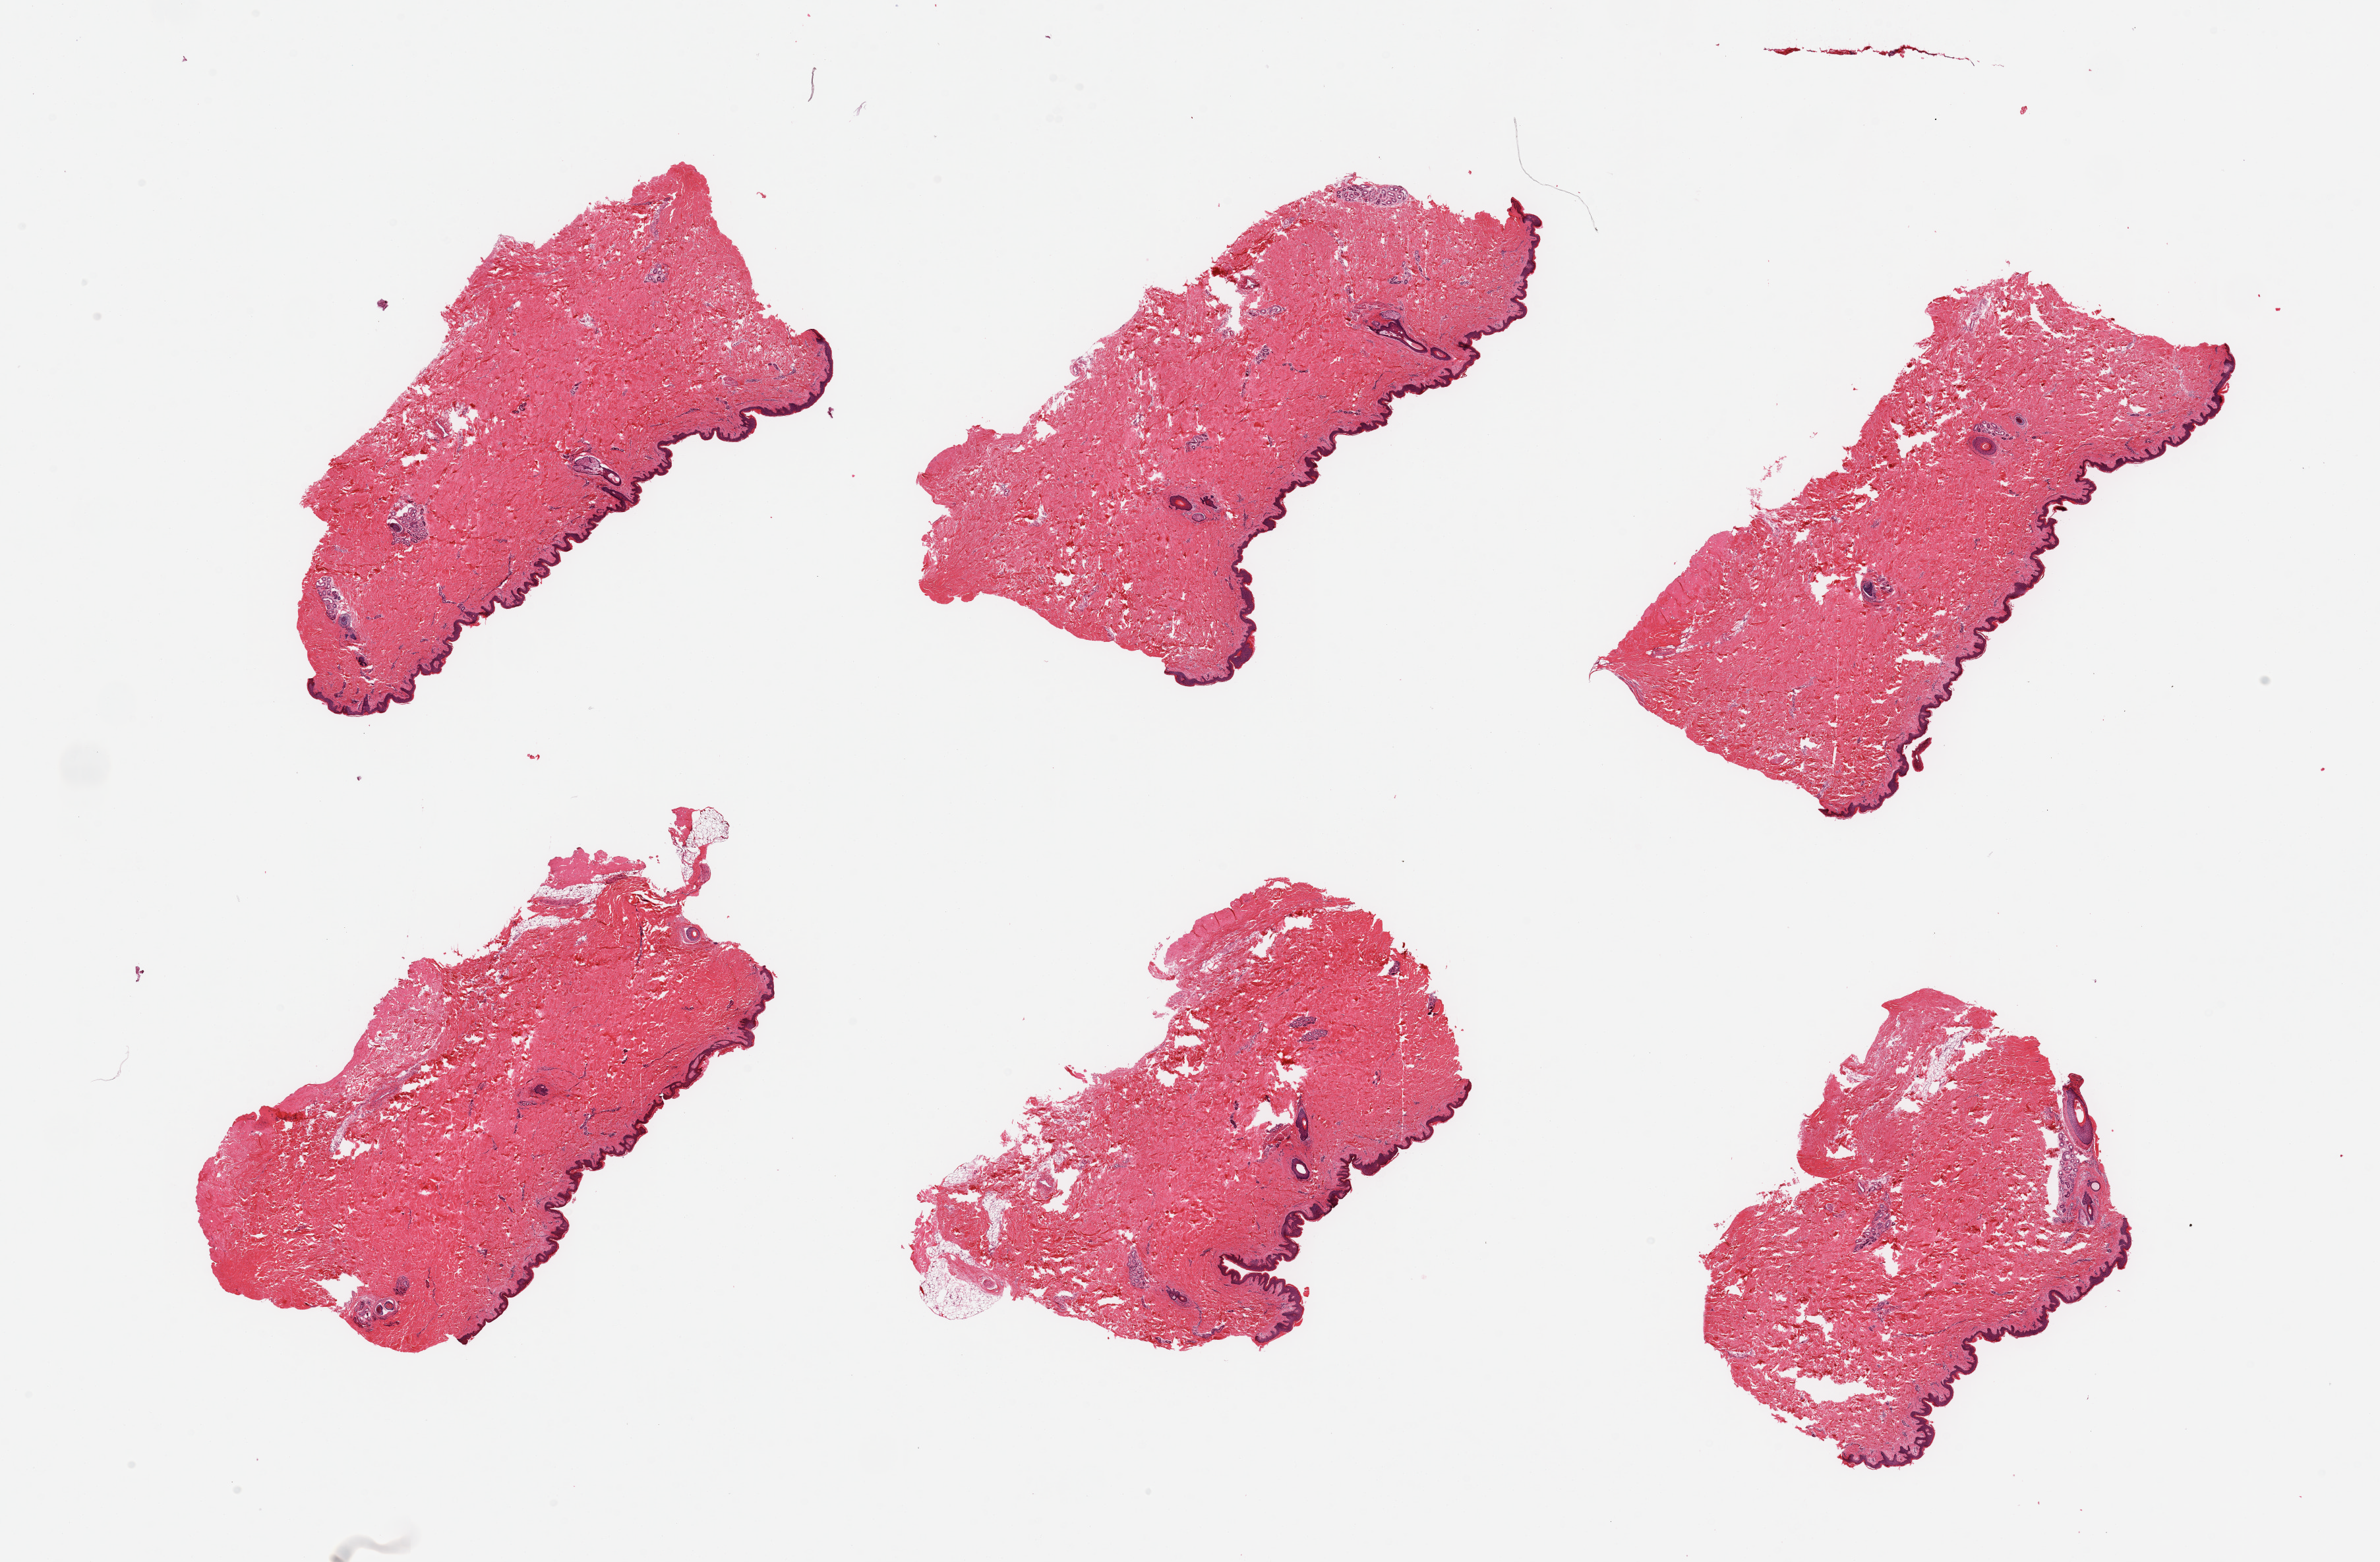
H&E whole-slide image — a low-resolution overview of the entire scanned area, about 28.5 x 18.7 mm; PAXgene-fixed paraffin-embedded (PFPE) section; target tissue: skin of suprapubic region; tissue donor sample. Donor sex: male.
Review note (as recorded): 6 pieces; relatively well trimmed.